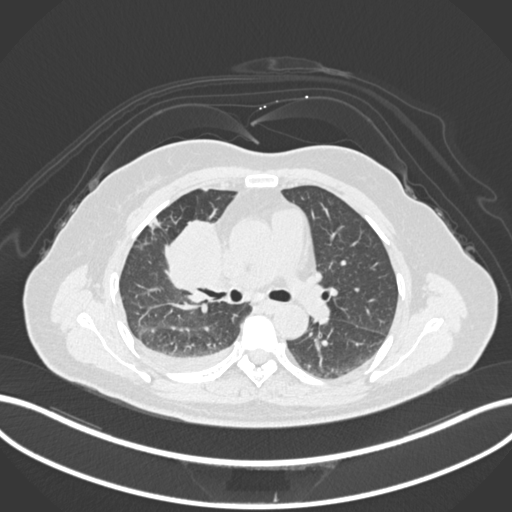
Chest CT, one axial slice. Position 87 of 172 along the scan axis. Reconstruction kernel B30f. 120 kVp. Lung window (W 1500 / L -600 HU). 1 mm slice thickness. 512 × 512 image matrix, field of view 400 × 400 mm. Female patient, age 52 years. From the clinical record (not read from this slice): clinical TNM (as recorded): T3 N1 M1.
Annotated regions visible in this slice (bounding box drawn by a radiologist):
- lung tumour (recorded histology: adenocarcinoma): box from (x=165, y=214) to (x=223, y=294) px